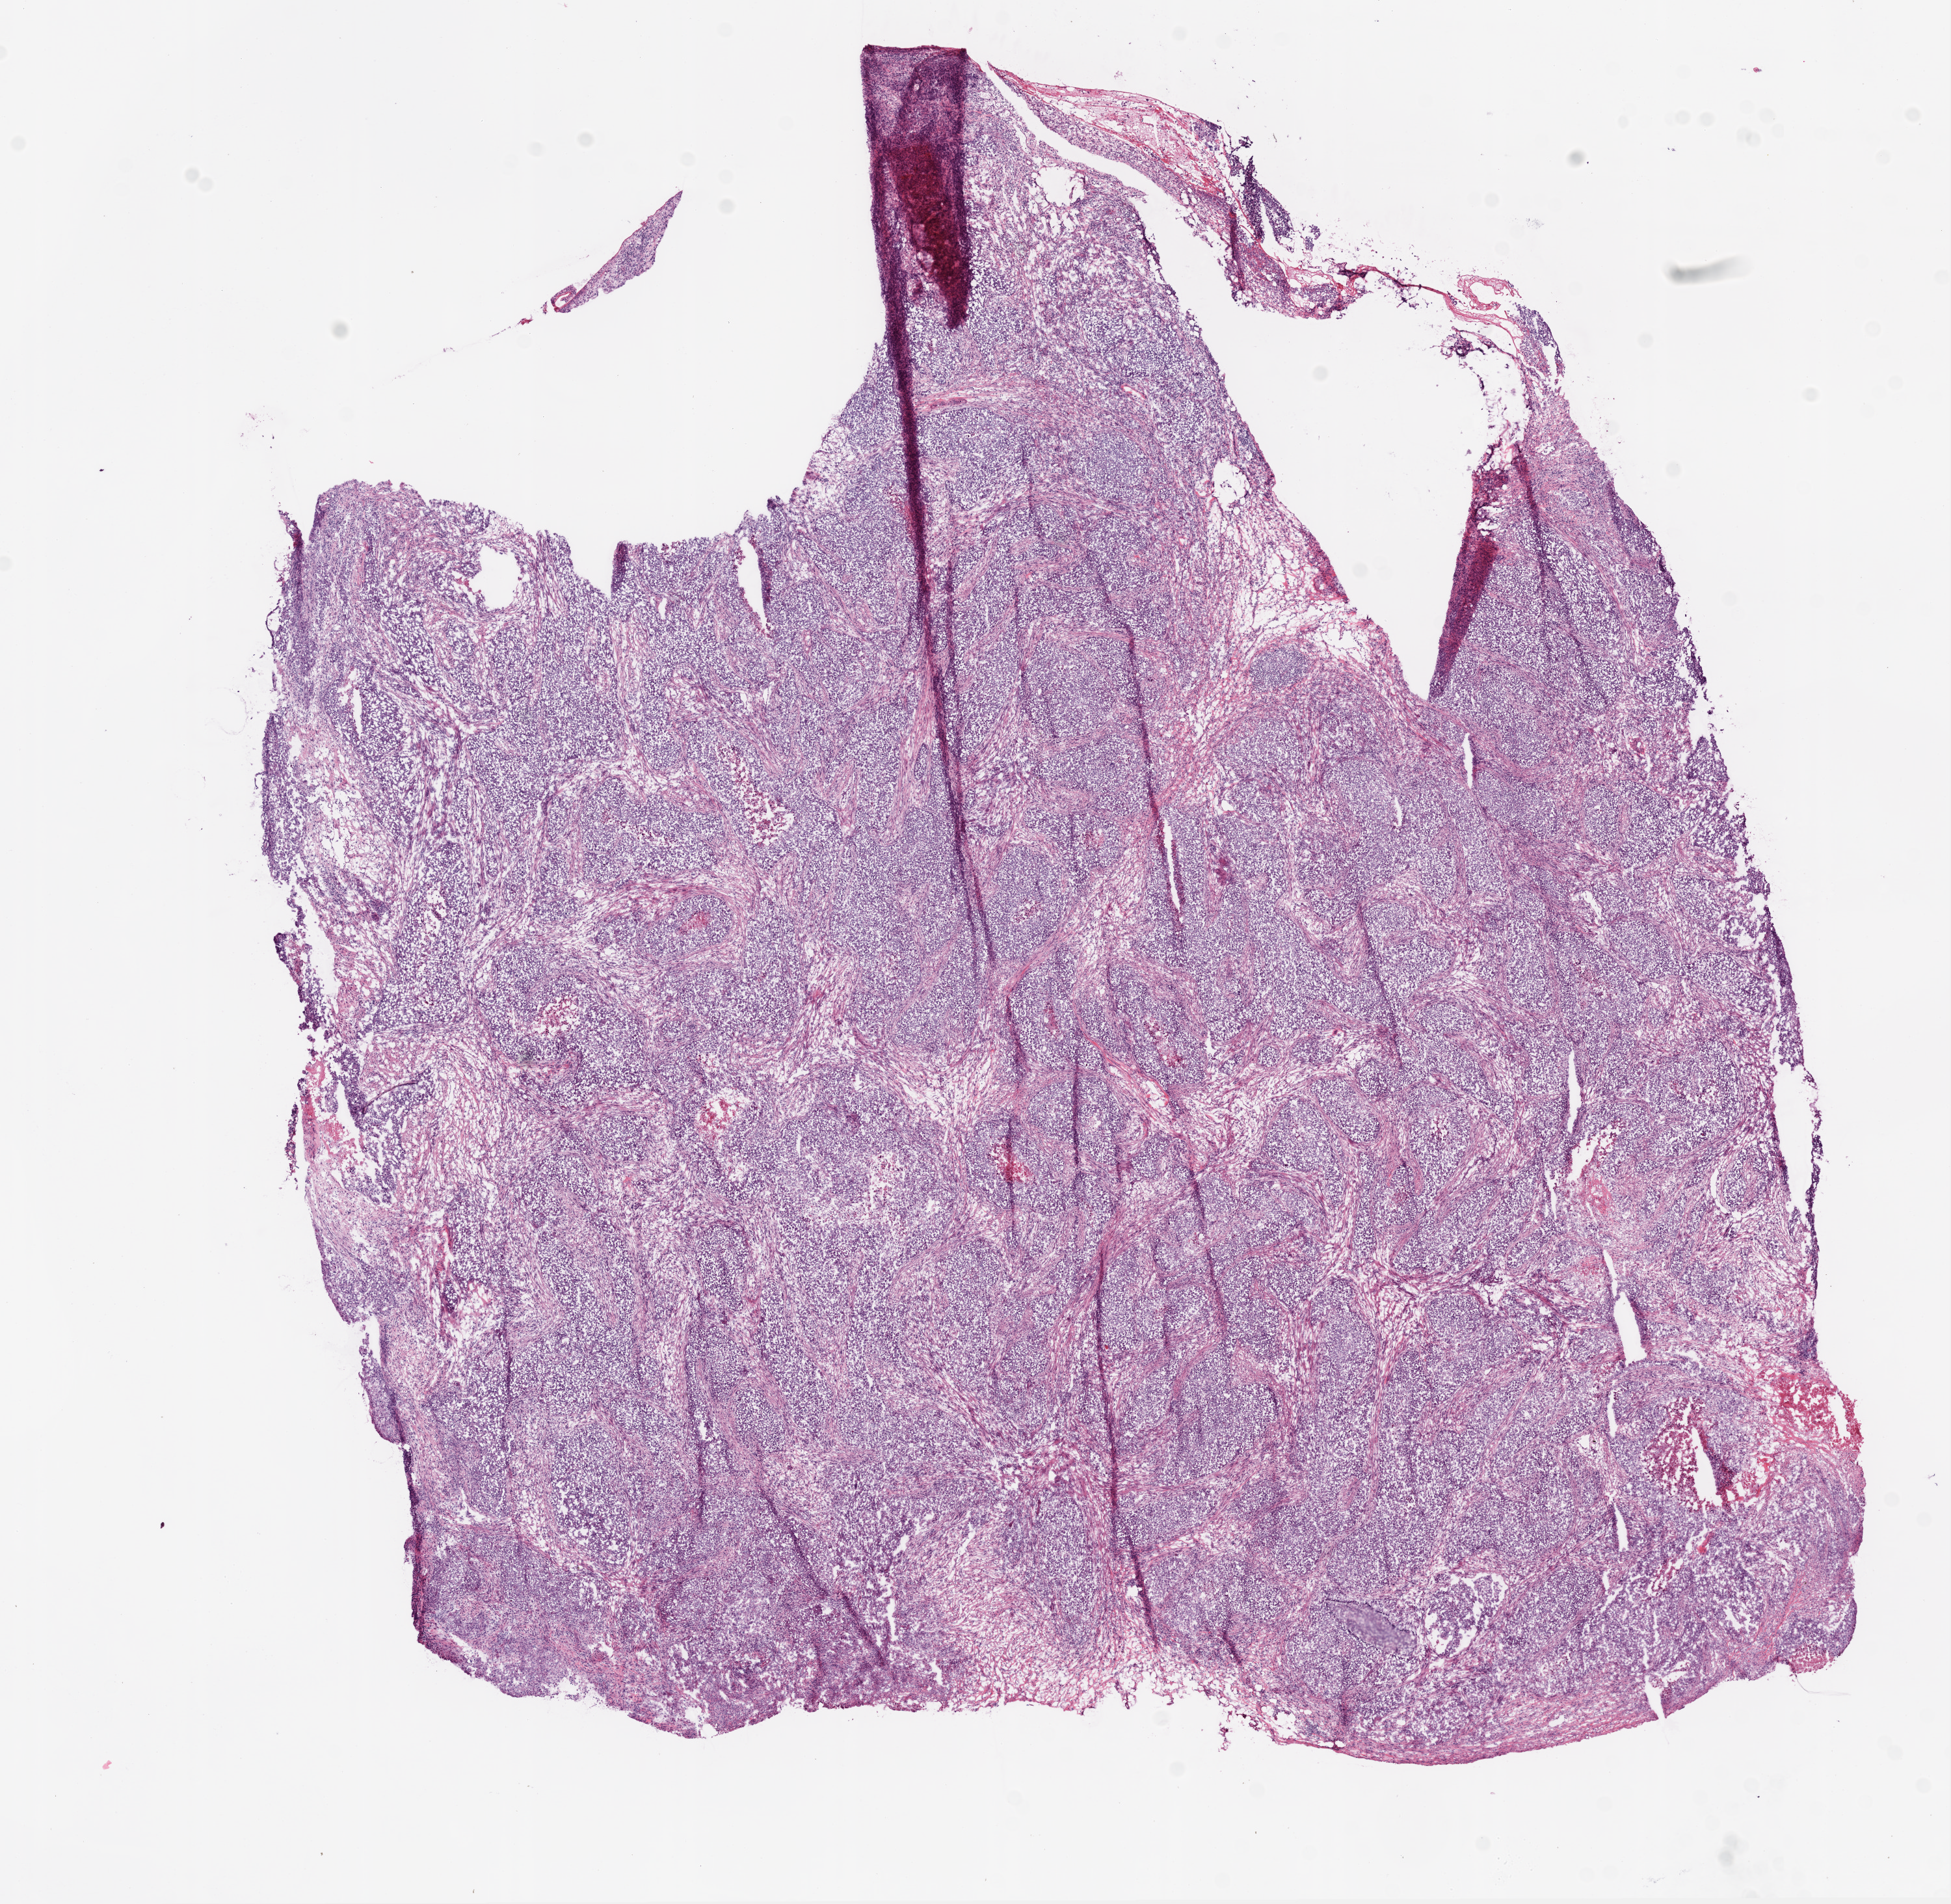
Hematoxylin and eosin (H&E) stained whole-slide image — whole scanned area (about 12.0 x 11.7 mm, slide scanned at 20x) shown as a low-resolution overview, frozen section, ovary, primary tumour sample. Patient: female, age at initial diagnosis 61 years. Histologic grade: G3 (poorly differentiated). Slide review estimates, as recorded: tumour cells 90%, tumour nuclei 90%, normal cells 0%, stromal cells 8%, necrosis 2%.
* FIGO stage: IIIC
* diagnosis: Serous cystadenocarcinoma, NOS